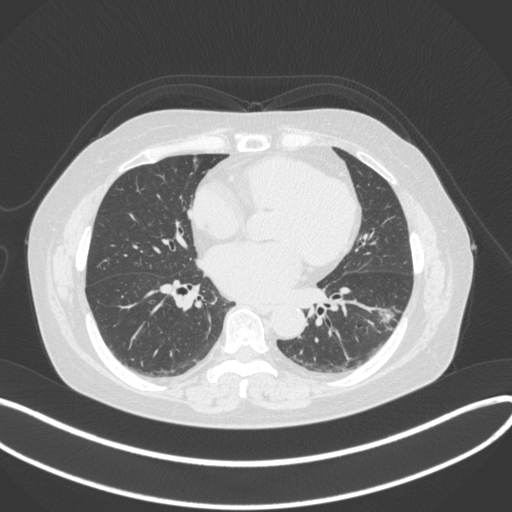
Chest CT, one axial slice; slice 157 of 373 in the series (ordered by position); reconstruction kernel B31f; 120 kVp; lung window (W 1500 / L -600 HU); 512 × 512 image matrix. Patient: female, 67 years. Case-level facts recorded for this patient, not image findings: clinical TNM (as recorded): T1c N0 M0; histopathological grade: G2.
Structures marked on this image (bounding box drawn by a radiologist):
- lung tumour (recorded histology: adenocarcinoma): bounding box [x1, y1, x2, y2] px = [372, 303, 406, 332]